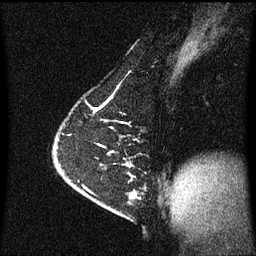
Breast MRI (dynamic contrast-enhanced), one sagittal slice. Slice 38 of 60 in the series (ordered by position). Dynamic contrast-enhanced series, image 2 of 3 at this slice position (ordered by acquisition). 1.5 T. TE 4.2 ms, TR 8.4 ms. 2 mm slice thickness. 256 × 256 image matrix. Patient: female, 63 years.
Structures marked on this image (semi-automatic segmentation, software-assisted and operator-edited):
- analysis volume of interest (the breast-tissue region the enhancement analysis was run in; not a lesion): bounding box (x1, y1, x2, y2) in pixels: (98, 174, 141, 217)
- tumour enhancement mask (voxels above the 70 % enhancement threshold inside the analysis volume of interest): (130, 192, 139, 199)